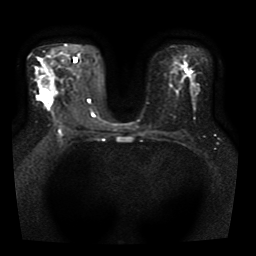
Breast MRI, one axial slice. Position 25 of 41 along the scan axis. Diffusion-weighted series; image 2 of 4 stored at this slice position (different b-values; order by instance number). 1.5 T. 5 mm slice thickness. 256 × 256 image matrix. Female patient.
Annotated regions visible in this slice (manually delineated by an expert):
- tumour on diffusion-weighted imaging: box from (x=41, y=92) to (x=52, y=103) px